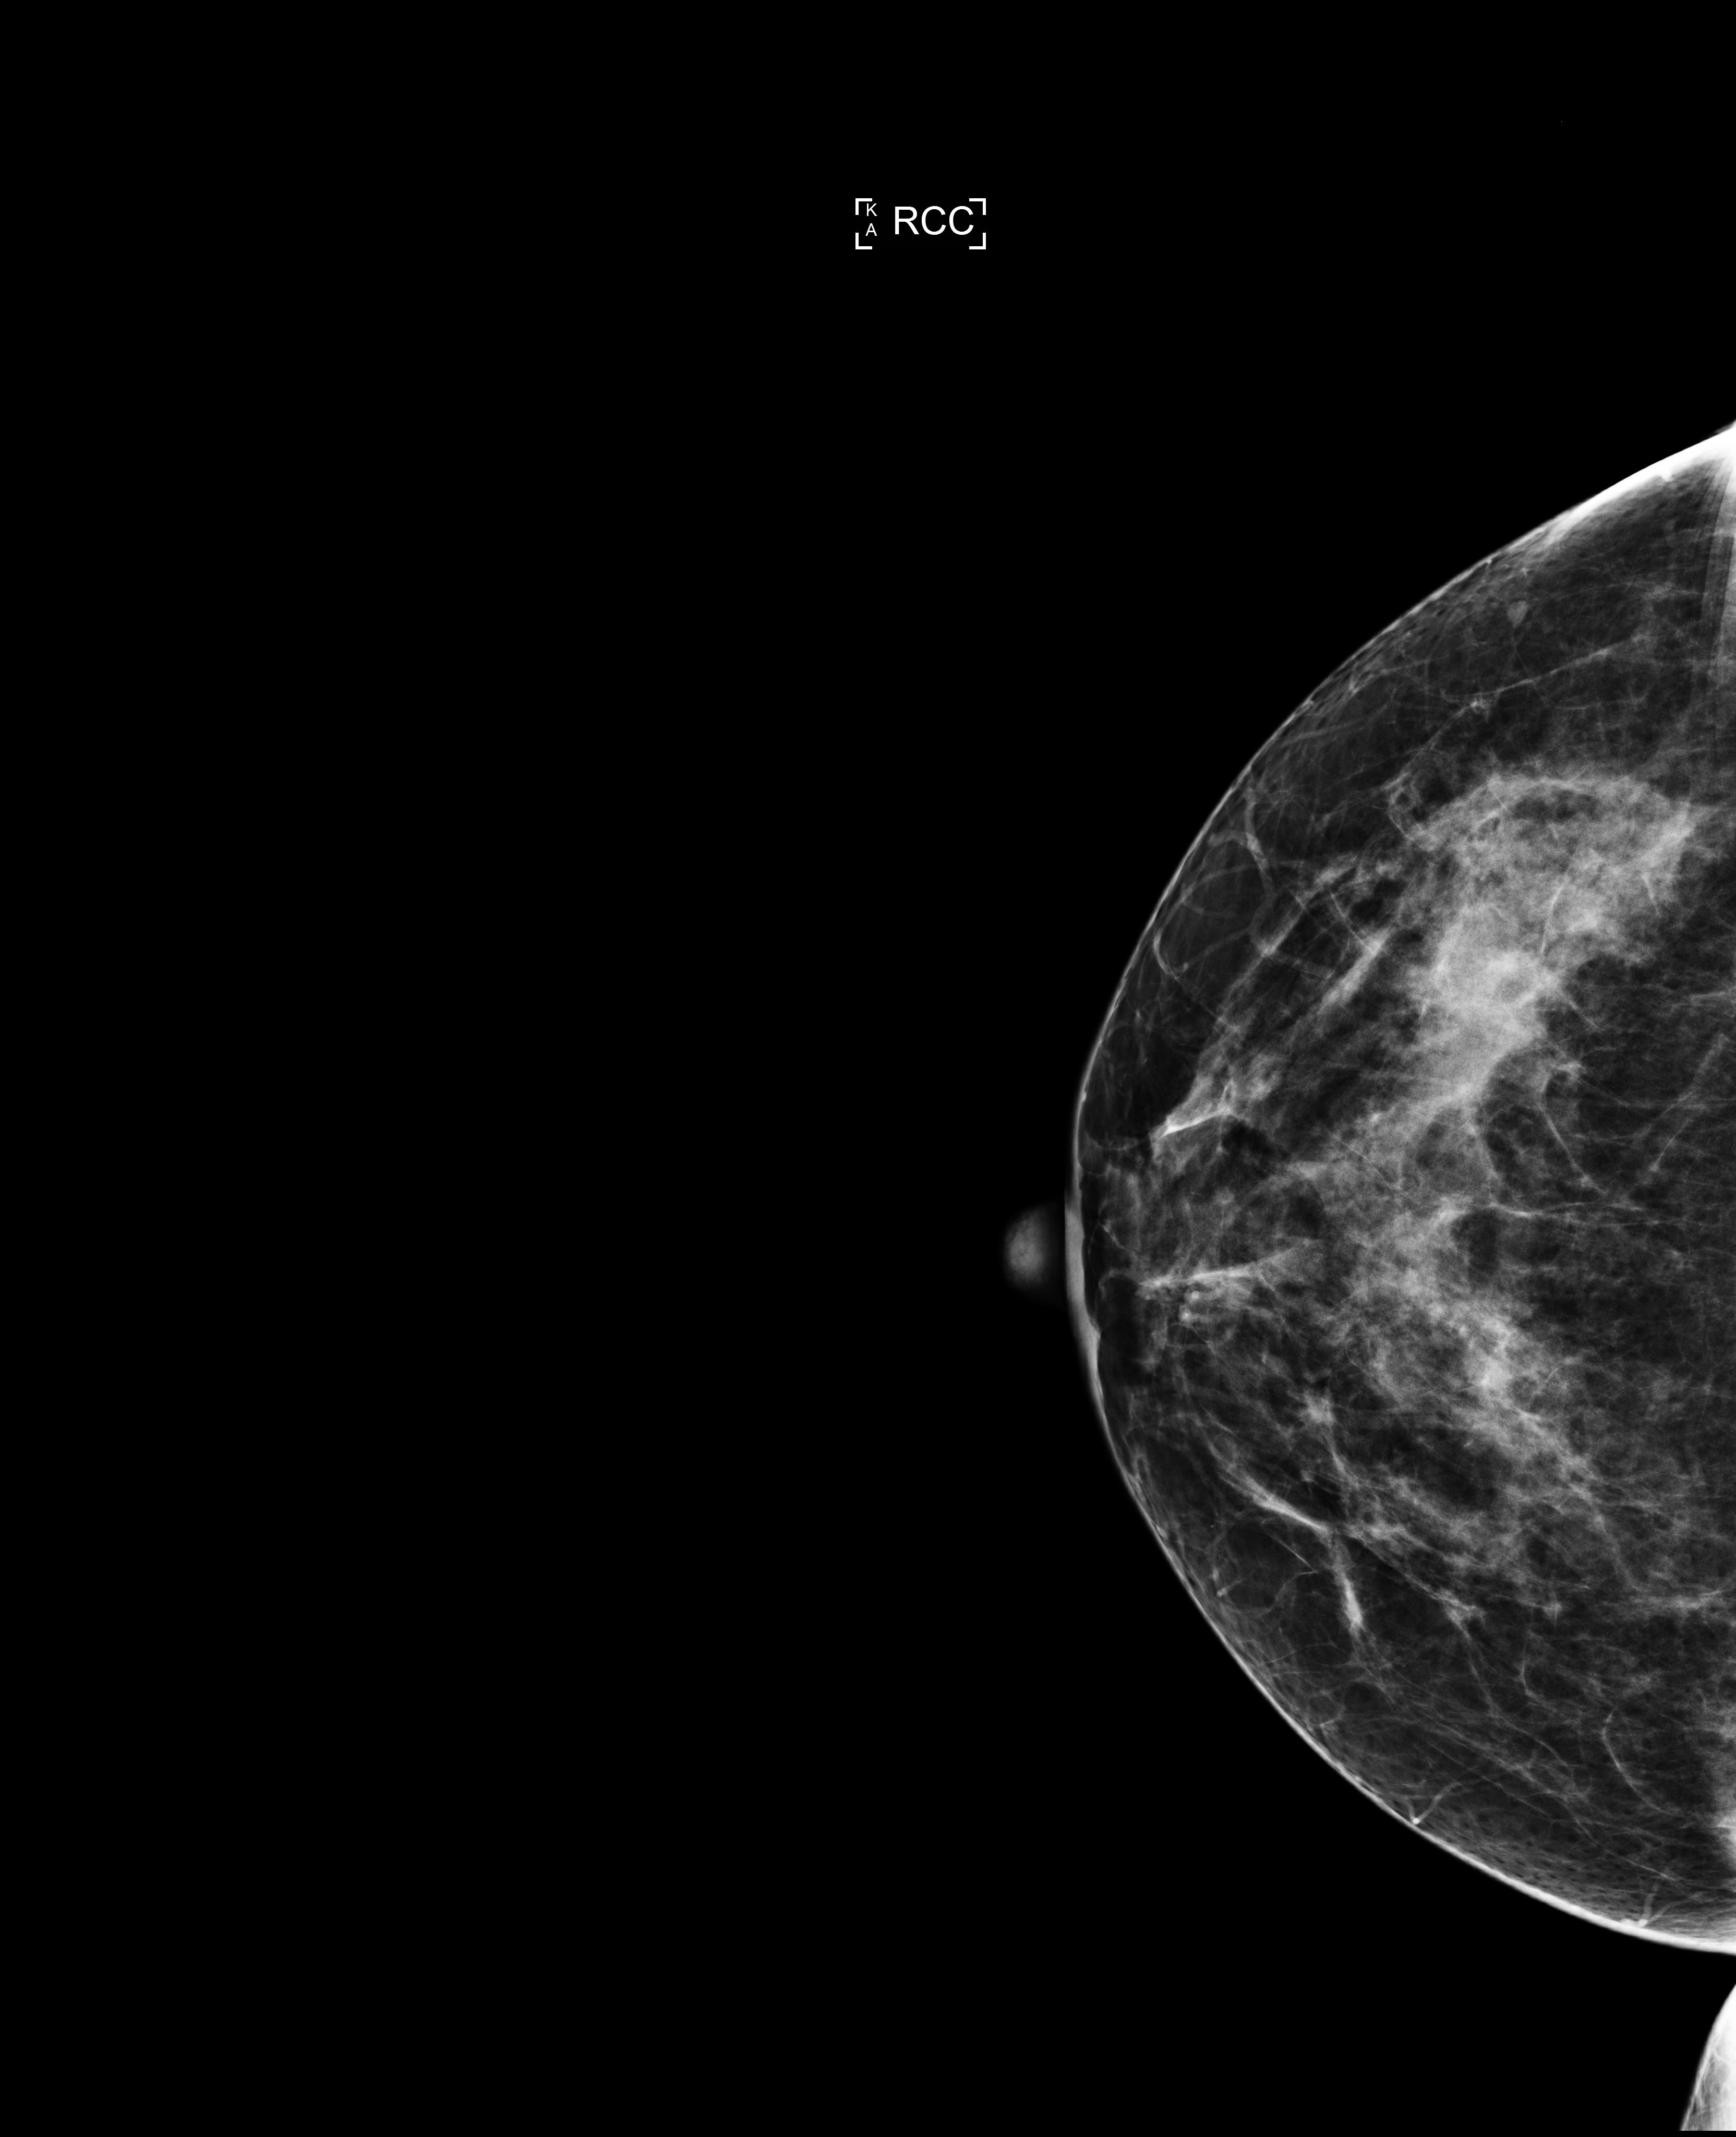
Annual screening mammography examination, compressed breast thickness 68 mm, system: Selenia Dimensions. Patient aged 47 years (female).
Image type: full-field digital mammogram. Breast: right. Projection: CC view.